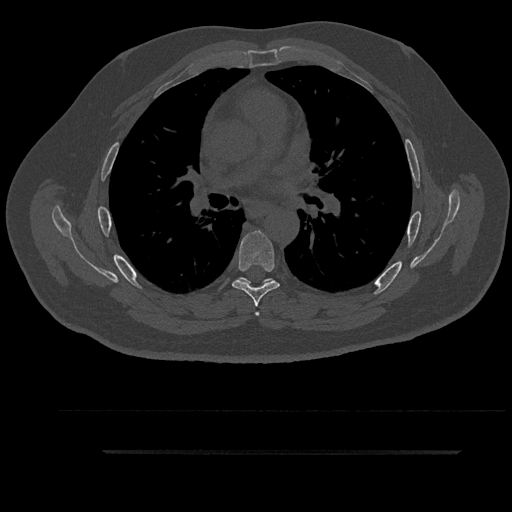
CT including the spine, one axial slice; position 575 of 797 along the scan axis; reconstruction kernel Br40s/3; bone window (W 1800 / L 400 HU); 512 × 512 image matrix, field of view 432 × 432 mm. Patient: male, 63 years. Case-level facts recorded for this patient, not image findings: primary cancer: renal.
Outlined on this slice (semi-automatically segmented with operator editing):
- T5 vertebra: bounding box [x1, y1, x2, y2] px = [236, 277, 273, 316]
- T6 vertebra: [232, 230, 280, 307]
- T7 vertebra: [244, 280, 273, 284]